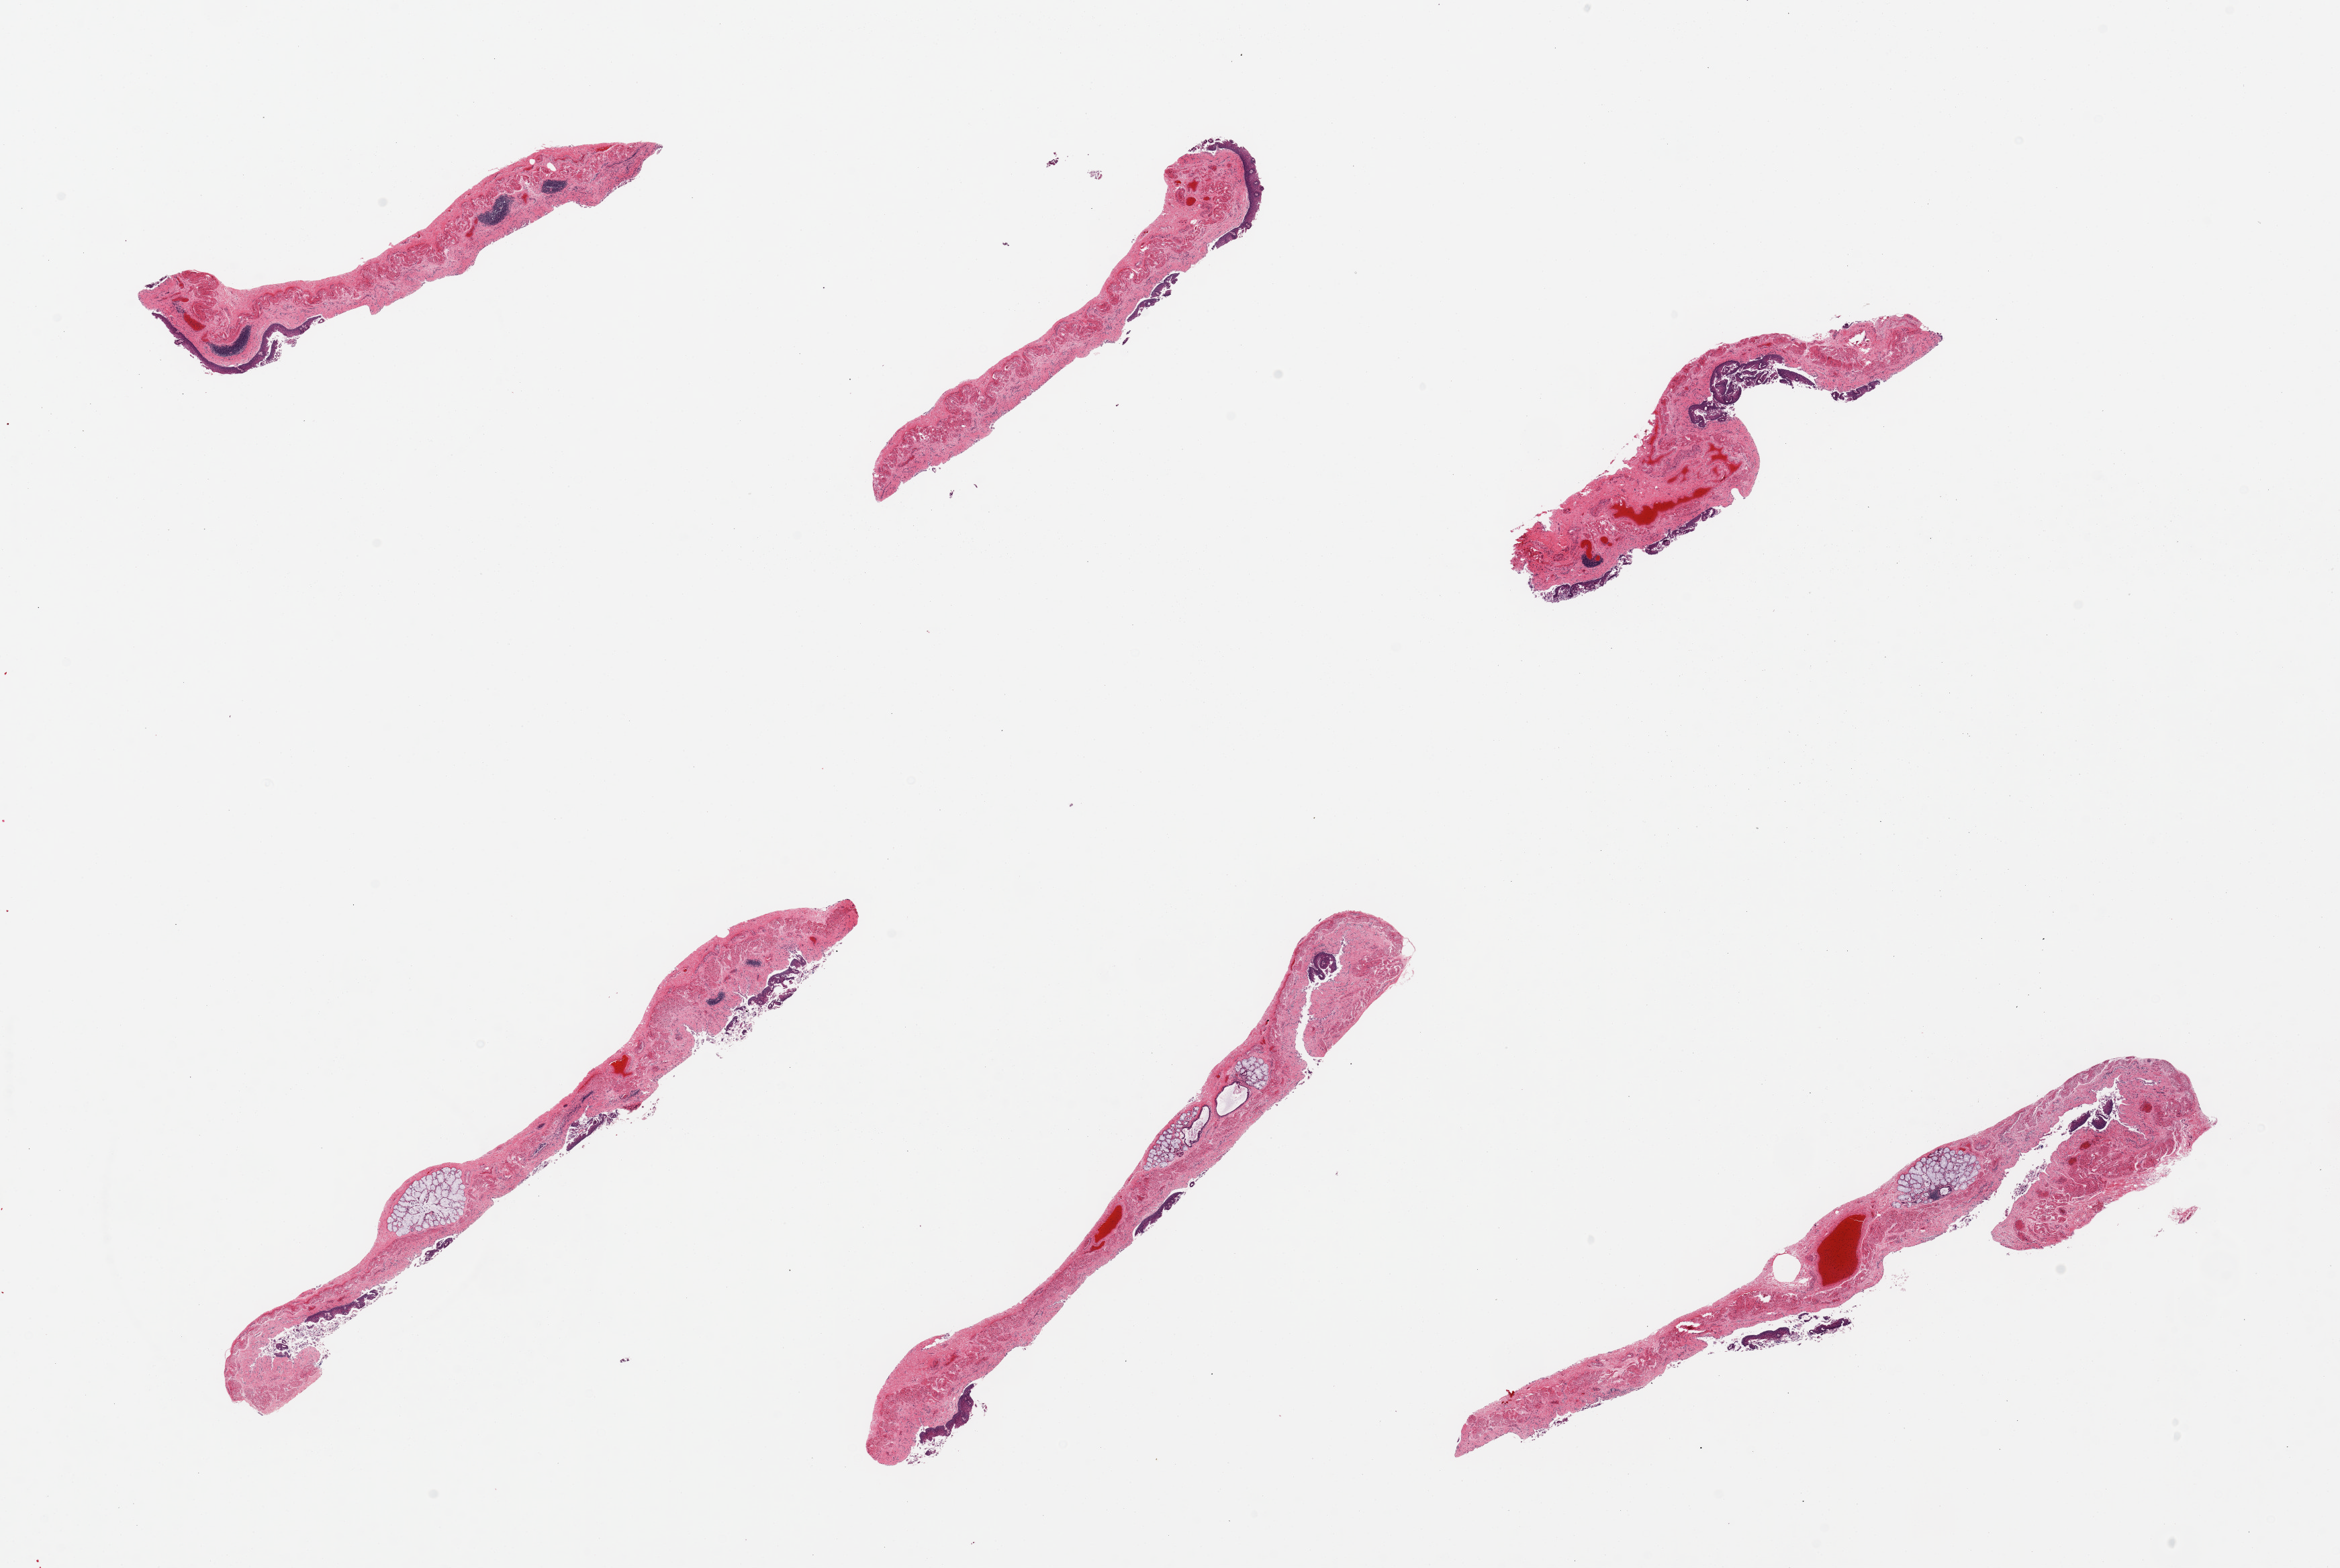
Whole-slide image, hematoxylin and eosin (H&E) stain — whole scanned area (about 27.6 x 18.5 mm) shown as a low-resolution overview.
Specimen: PAXgene-fixed paraffin-embedded (PFPE) section; sampled site (target tissue): esophageal mucous membrane; tissue donor sample.